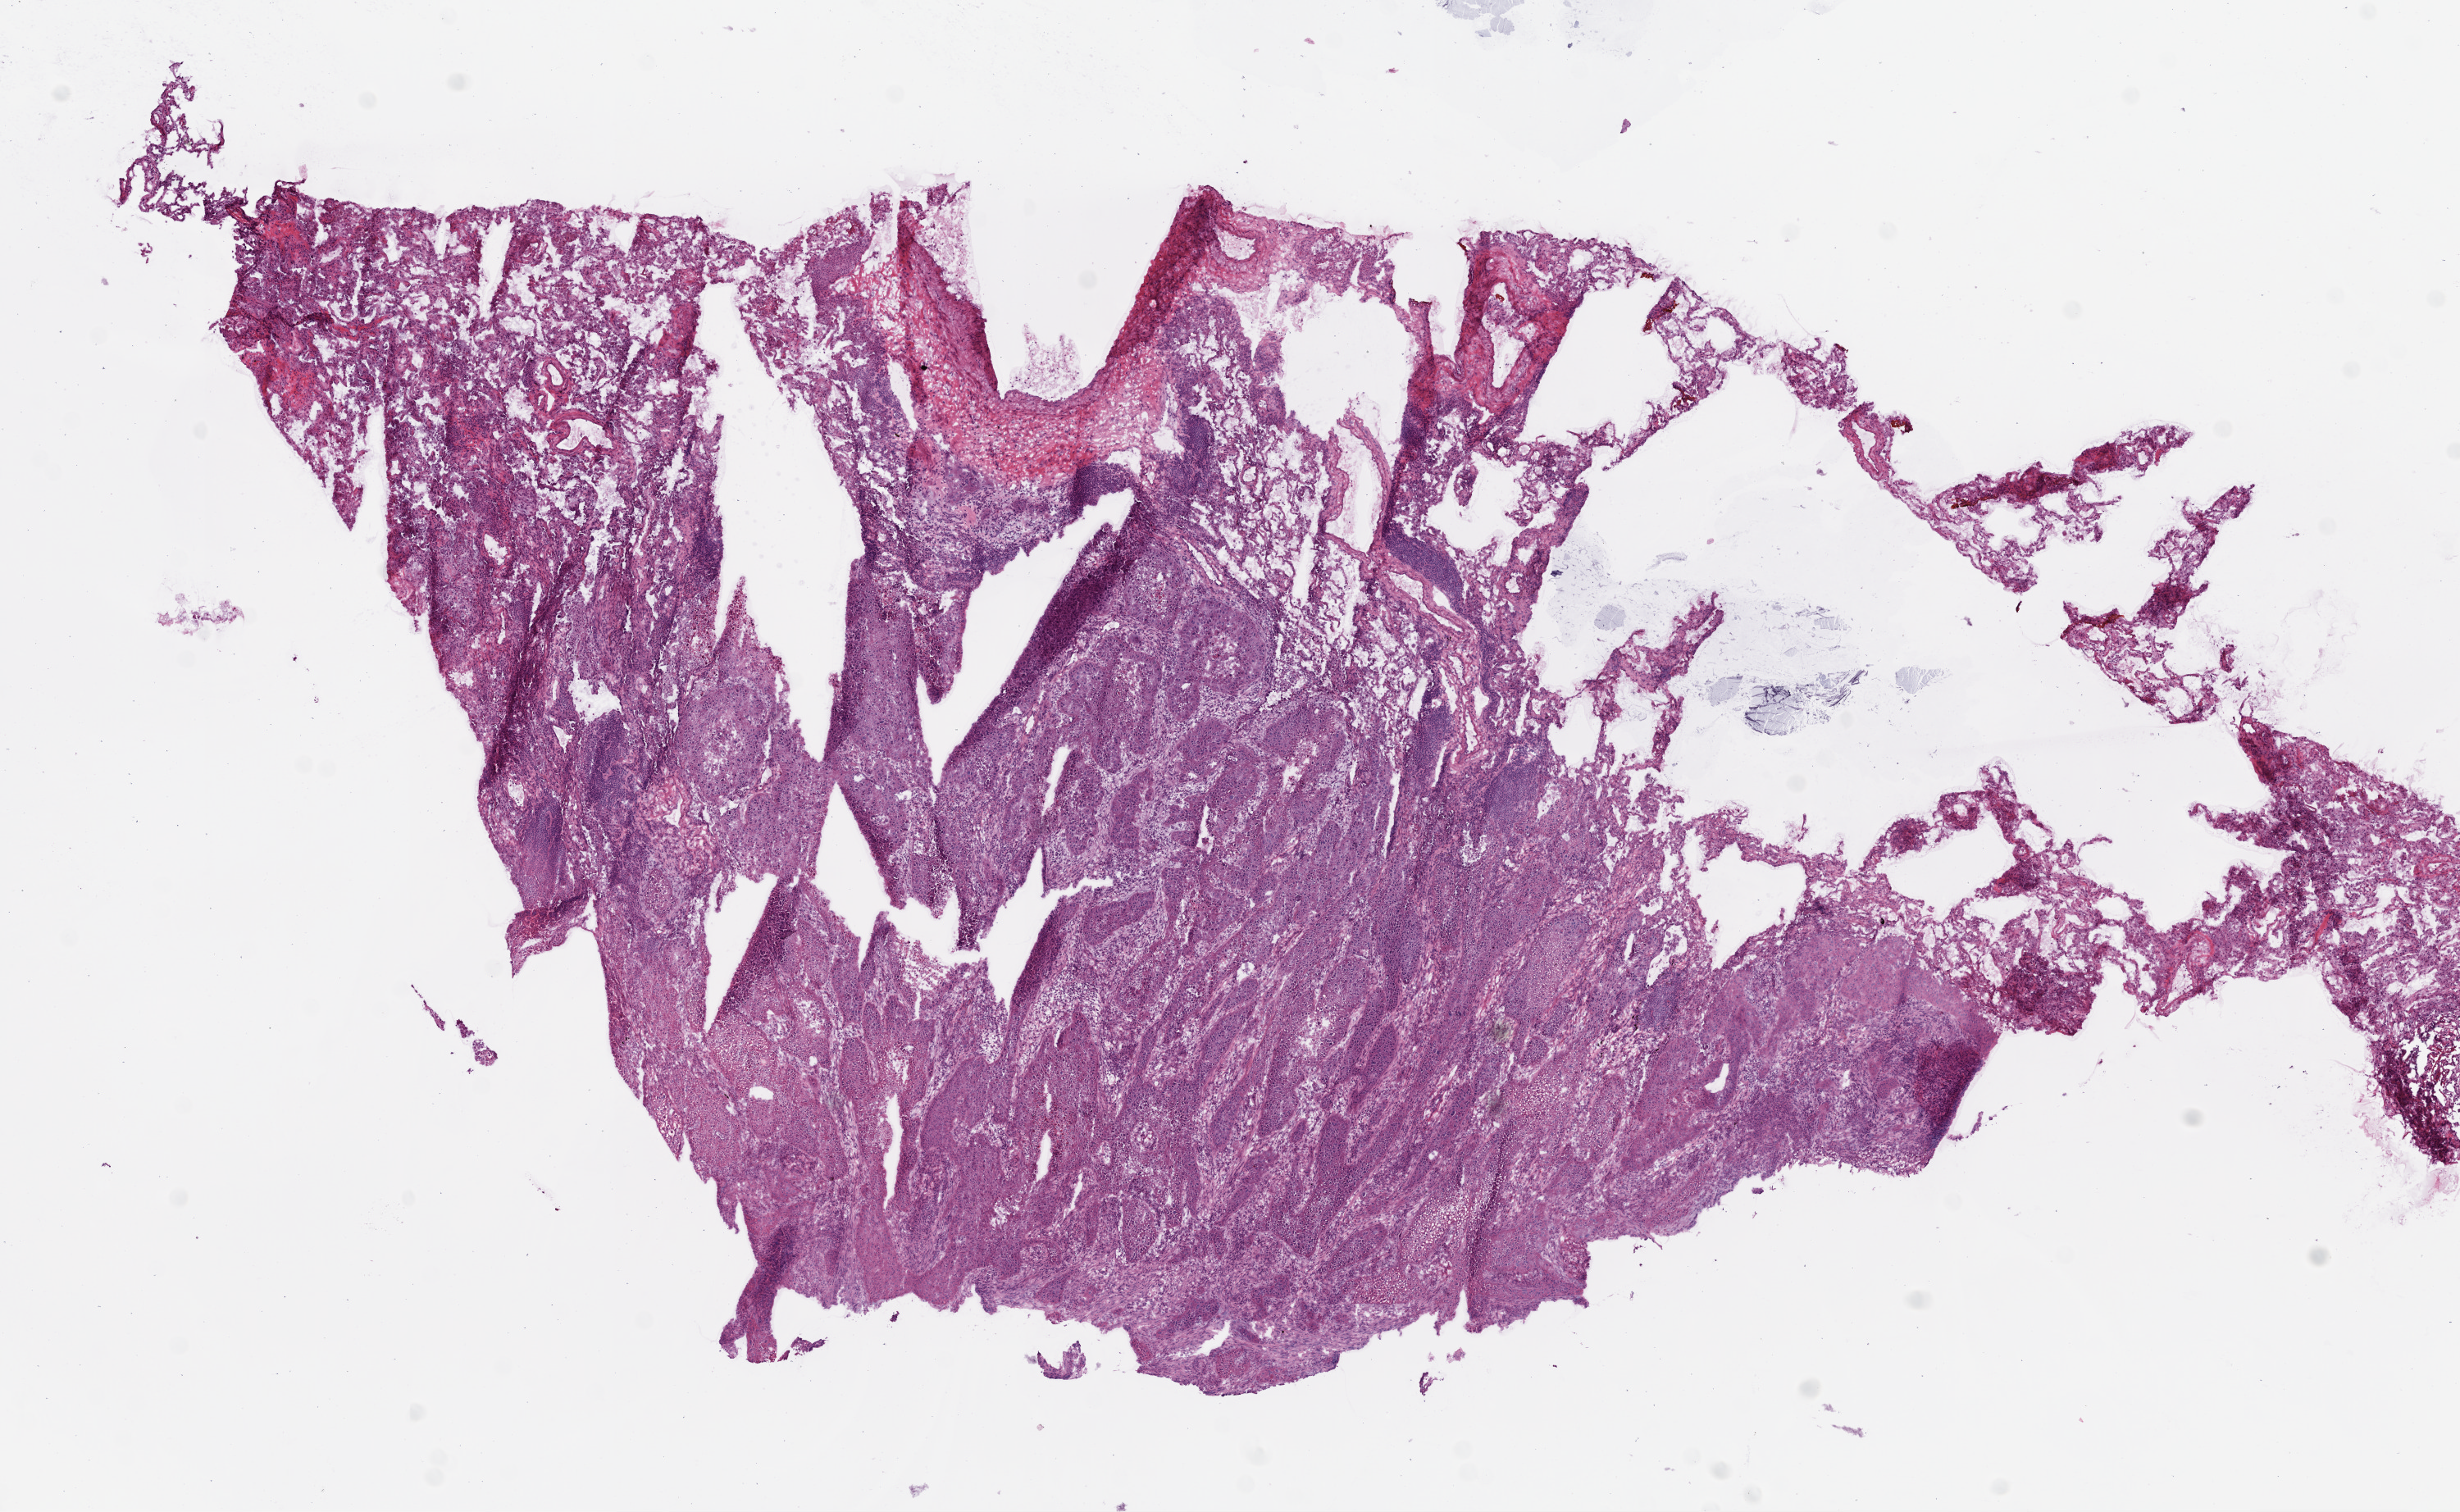
Digitized H&E tissue section (whole slide) — a low-resolution overview of the entire scanned area, about 12.0 x 7.4 mm (from a 20x scan), frozen section, lung, primary tumour sample. Female, age 67 years at initial diagnosis. Slide review estimates, as recorded: tumour cells 85%, tumour nuclei 70%, normal cells 0%, stromal cells 15%, necrosis 0%.
* laterality: right
* AJCC pathologic stage: IA
* pathologic diagnosis: Squamous cell carcinoma, NOS